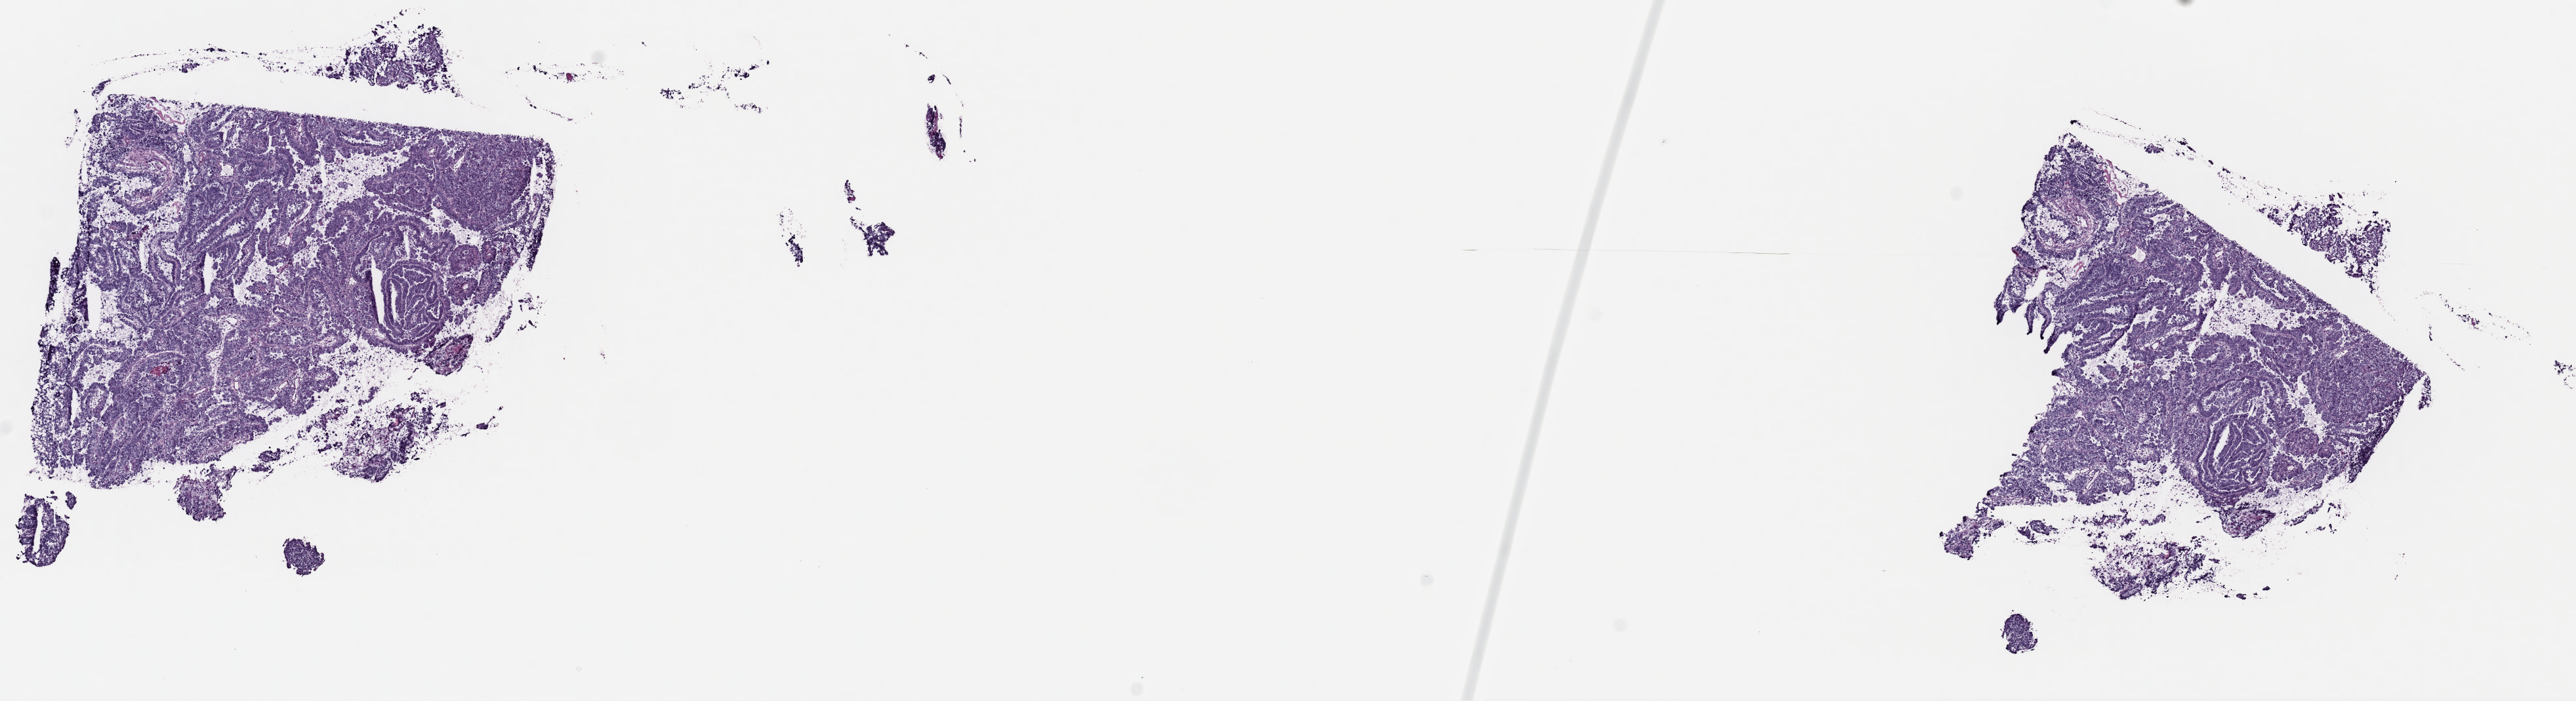
Digitized Hematoxylin and eosin (H&E) stained tissue section (whole slide) — low-resolution overview of the scanned area, about 15.5 x 4.2 mm. Frozen section from the top of the tissue portion. Sample: primary tumour, uterus. Female patient; age at initial diagnosis 83 years. Histologic grade: G3 (poorly differentiated). Pathologist review of this section (percent, as recorded): tumour cells 90%, tumour nuclei 90%, normal cells 0%, stromal cells 5%, necrosis 5%. Infiltration values recorded for this section: lymphocyte infiltration 40%, monocyte infiltration 20%, neutrophil infiltration 20%.
Lymph nodes positive (case pathology): 0 of 19 examined. FIGO stage: IIIC1. Diagnosis: Papillary serous cystadenocarcinoma (endometrium).